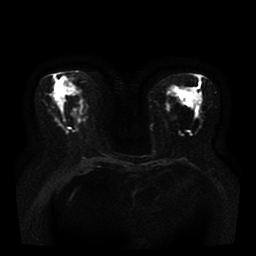
Breast MRI, one axial slice; slice 16 of 36 in the series (ordered by position); diffusion-weighted series; image 2 of 4 stored at this slice position (different b-values; order by instance number); 1.5 T; 5 mm slice thickness; 256 × 256 image matrix, field of view 330 × 330 mm. Female patient.
Annotated regions visible in this slice (outlined manually by an expert reader):
- tumour on diffusion-weighted imaging: box from (x=191, y=96) to (x=196, y=102) px